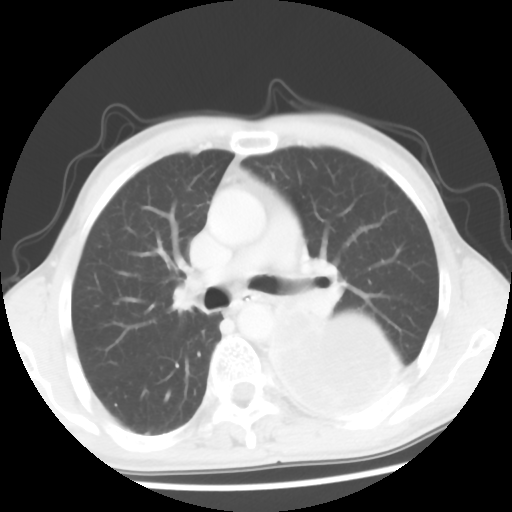
Chest CT, one axial slice. Position 35 of 56 along the scan axis. Reconstruction kernel STANDARD. 120 kVp. Lung window (W 1500 / L -600 HU). 5 mm slice thickness. 512 × 512 image matrix, field of view 318 × 318 mm. Patient: male, 60 years. Case-level facts recorded for this patient, not image findings: clinical TNM (as recorded): T4 N0 M0.
Annotated regions visible in this slice (rectangle marked by the reading radiologist):
- lung tumour (recorded histology: squamous cell carcinoma): bounding box (x1, y1, x2, y2) in pixels: (250, 301, 436, 442)